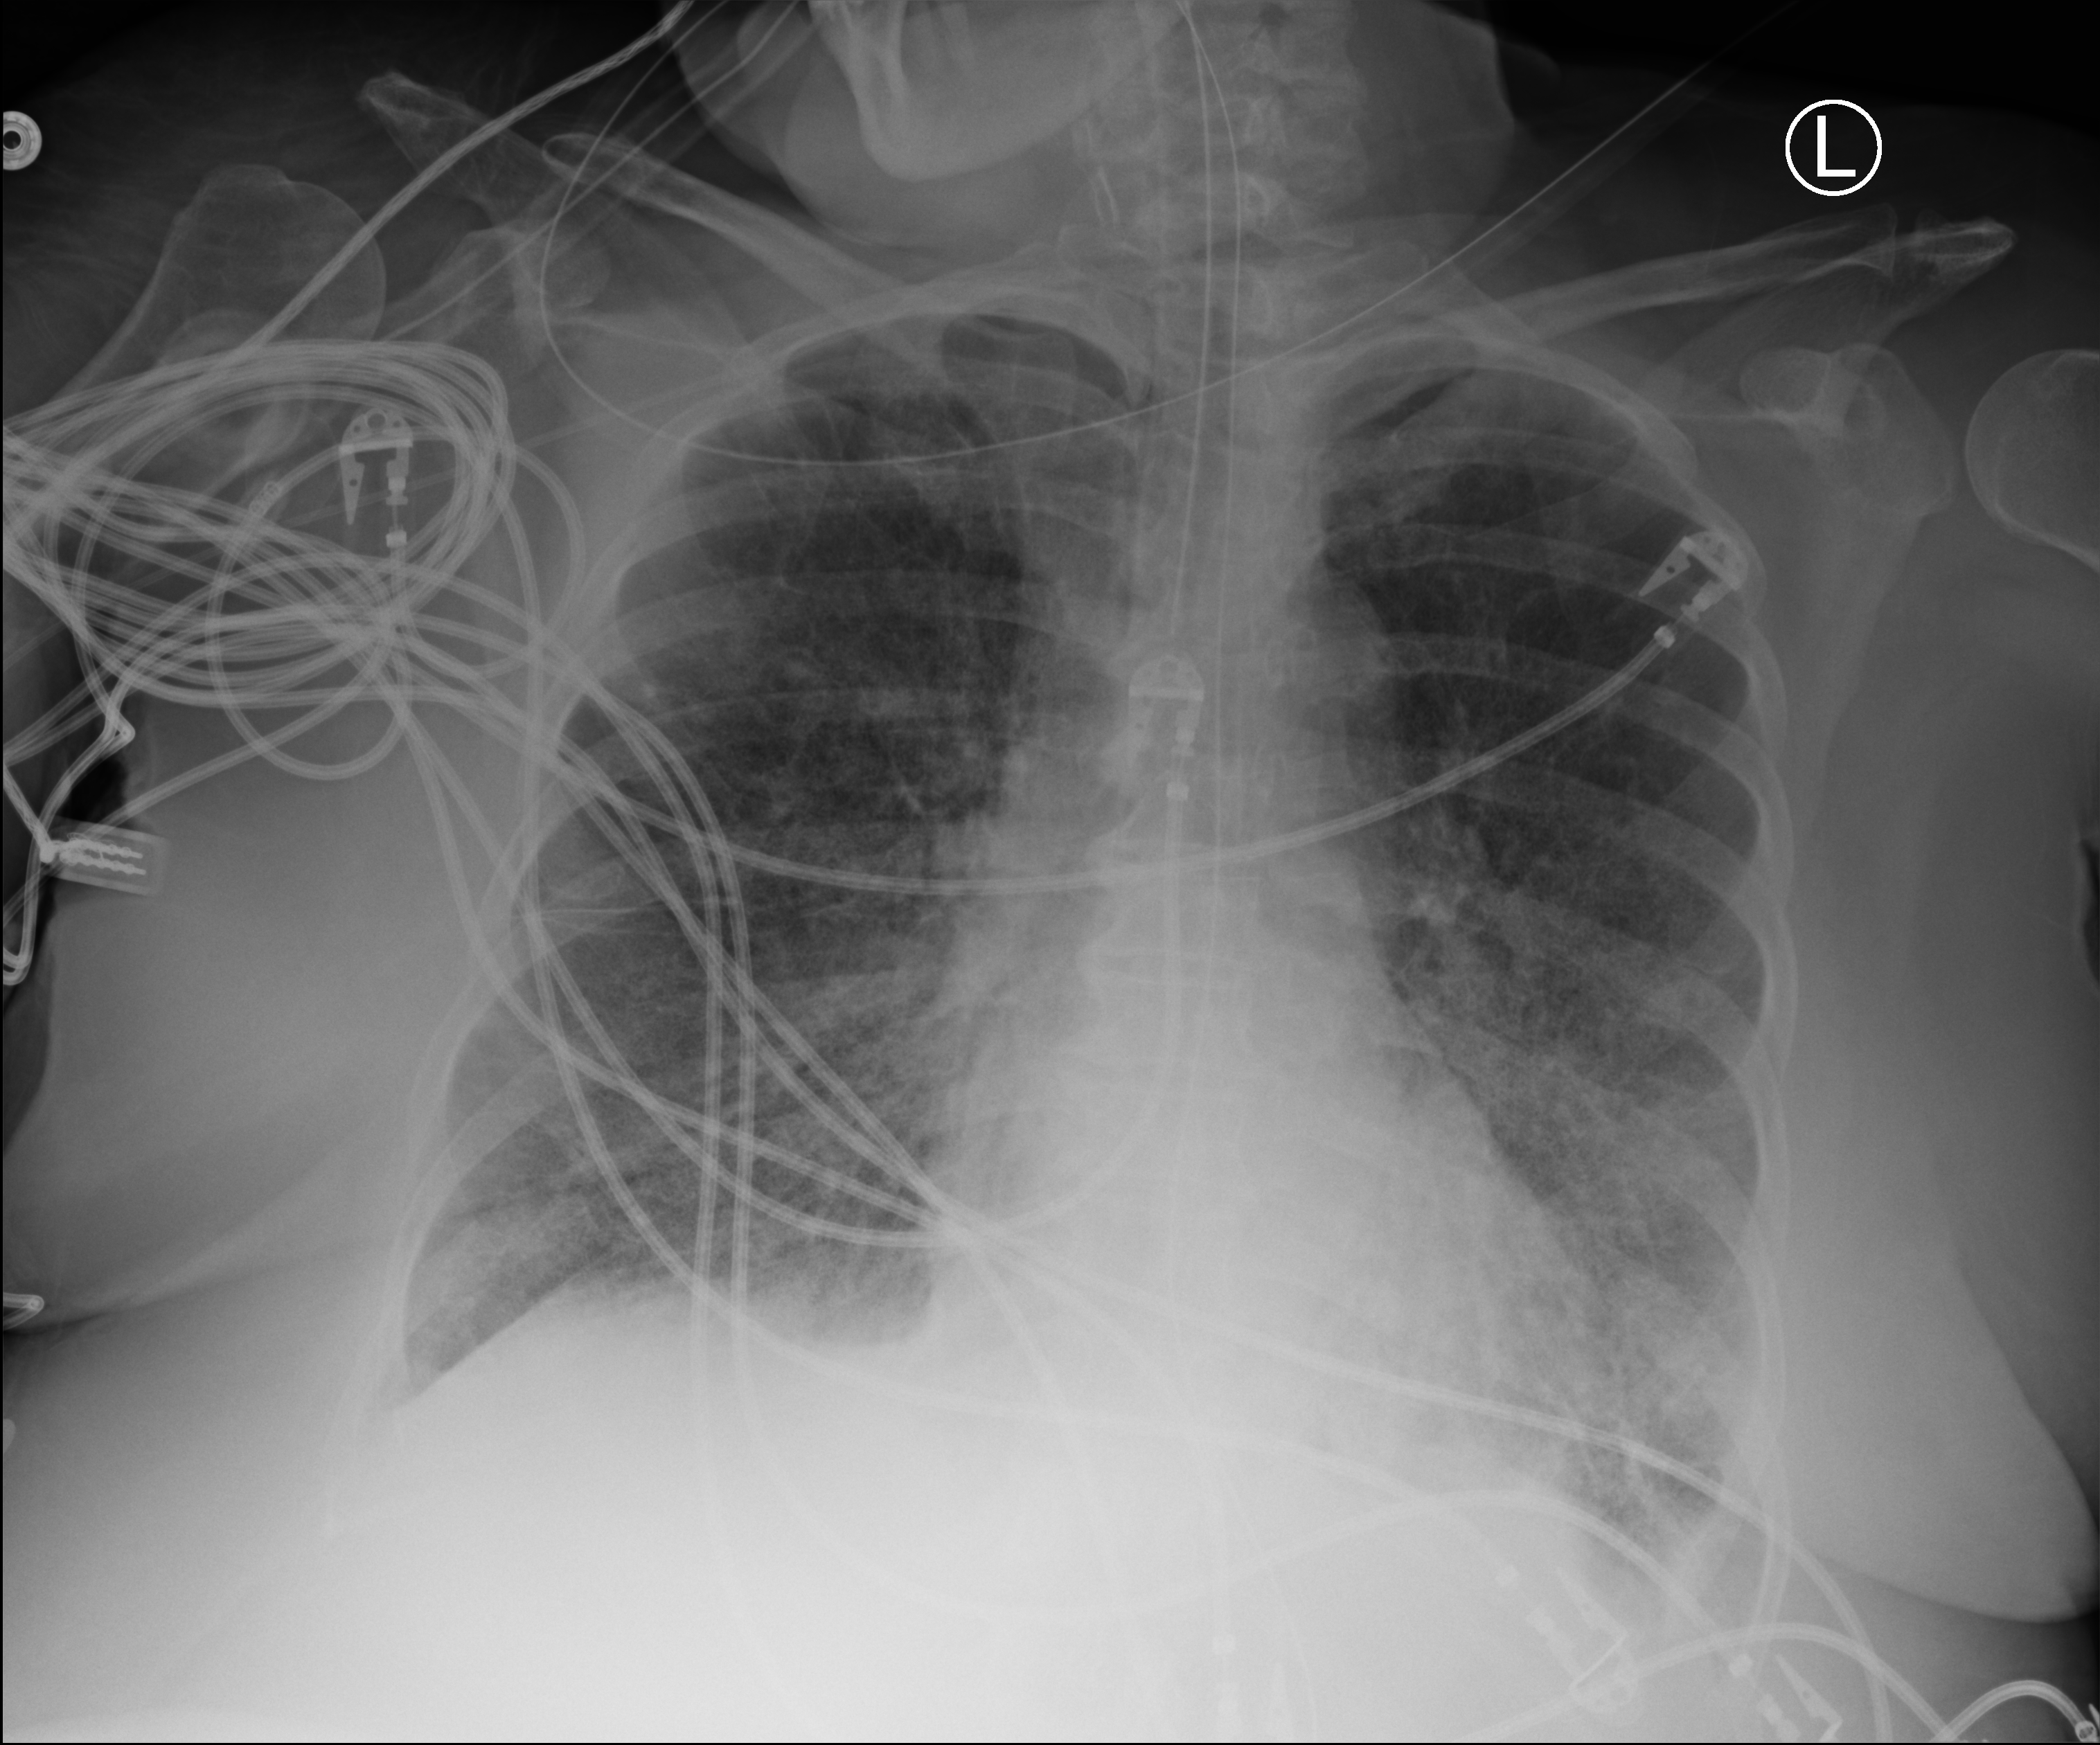
Portable chest radiograph. Patient hospitalised with COVID-19; female, aged 60–74 years.
Hospital-stay facts (about this admission, not read from this image; timing relative to this image not recorded): diabetes (admission record): no; mechanically ventilated during this hospital stay: yes.